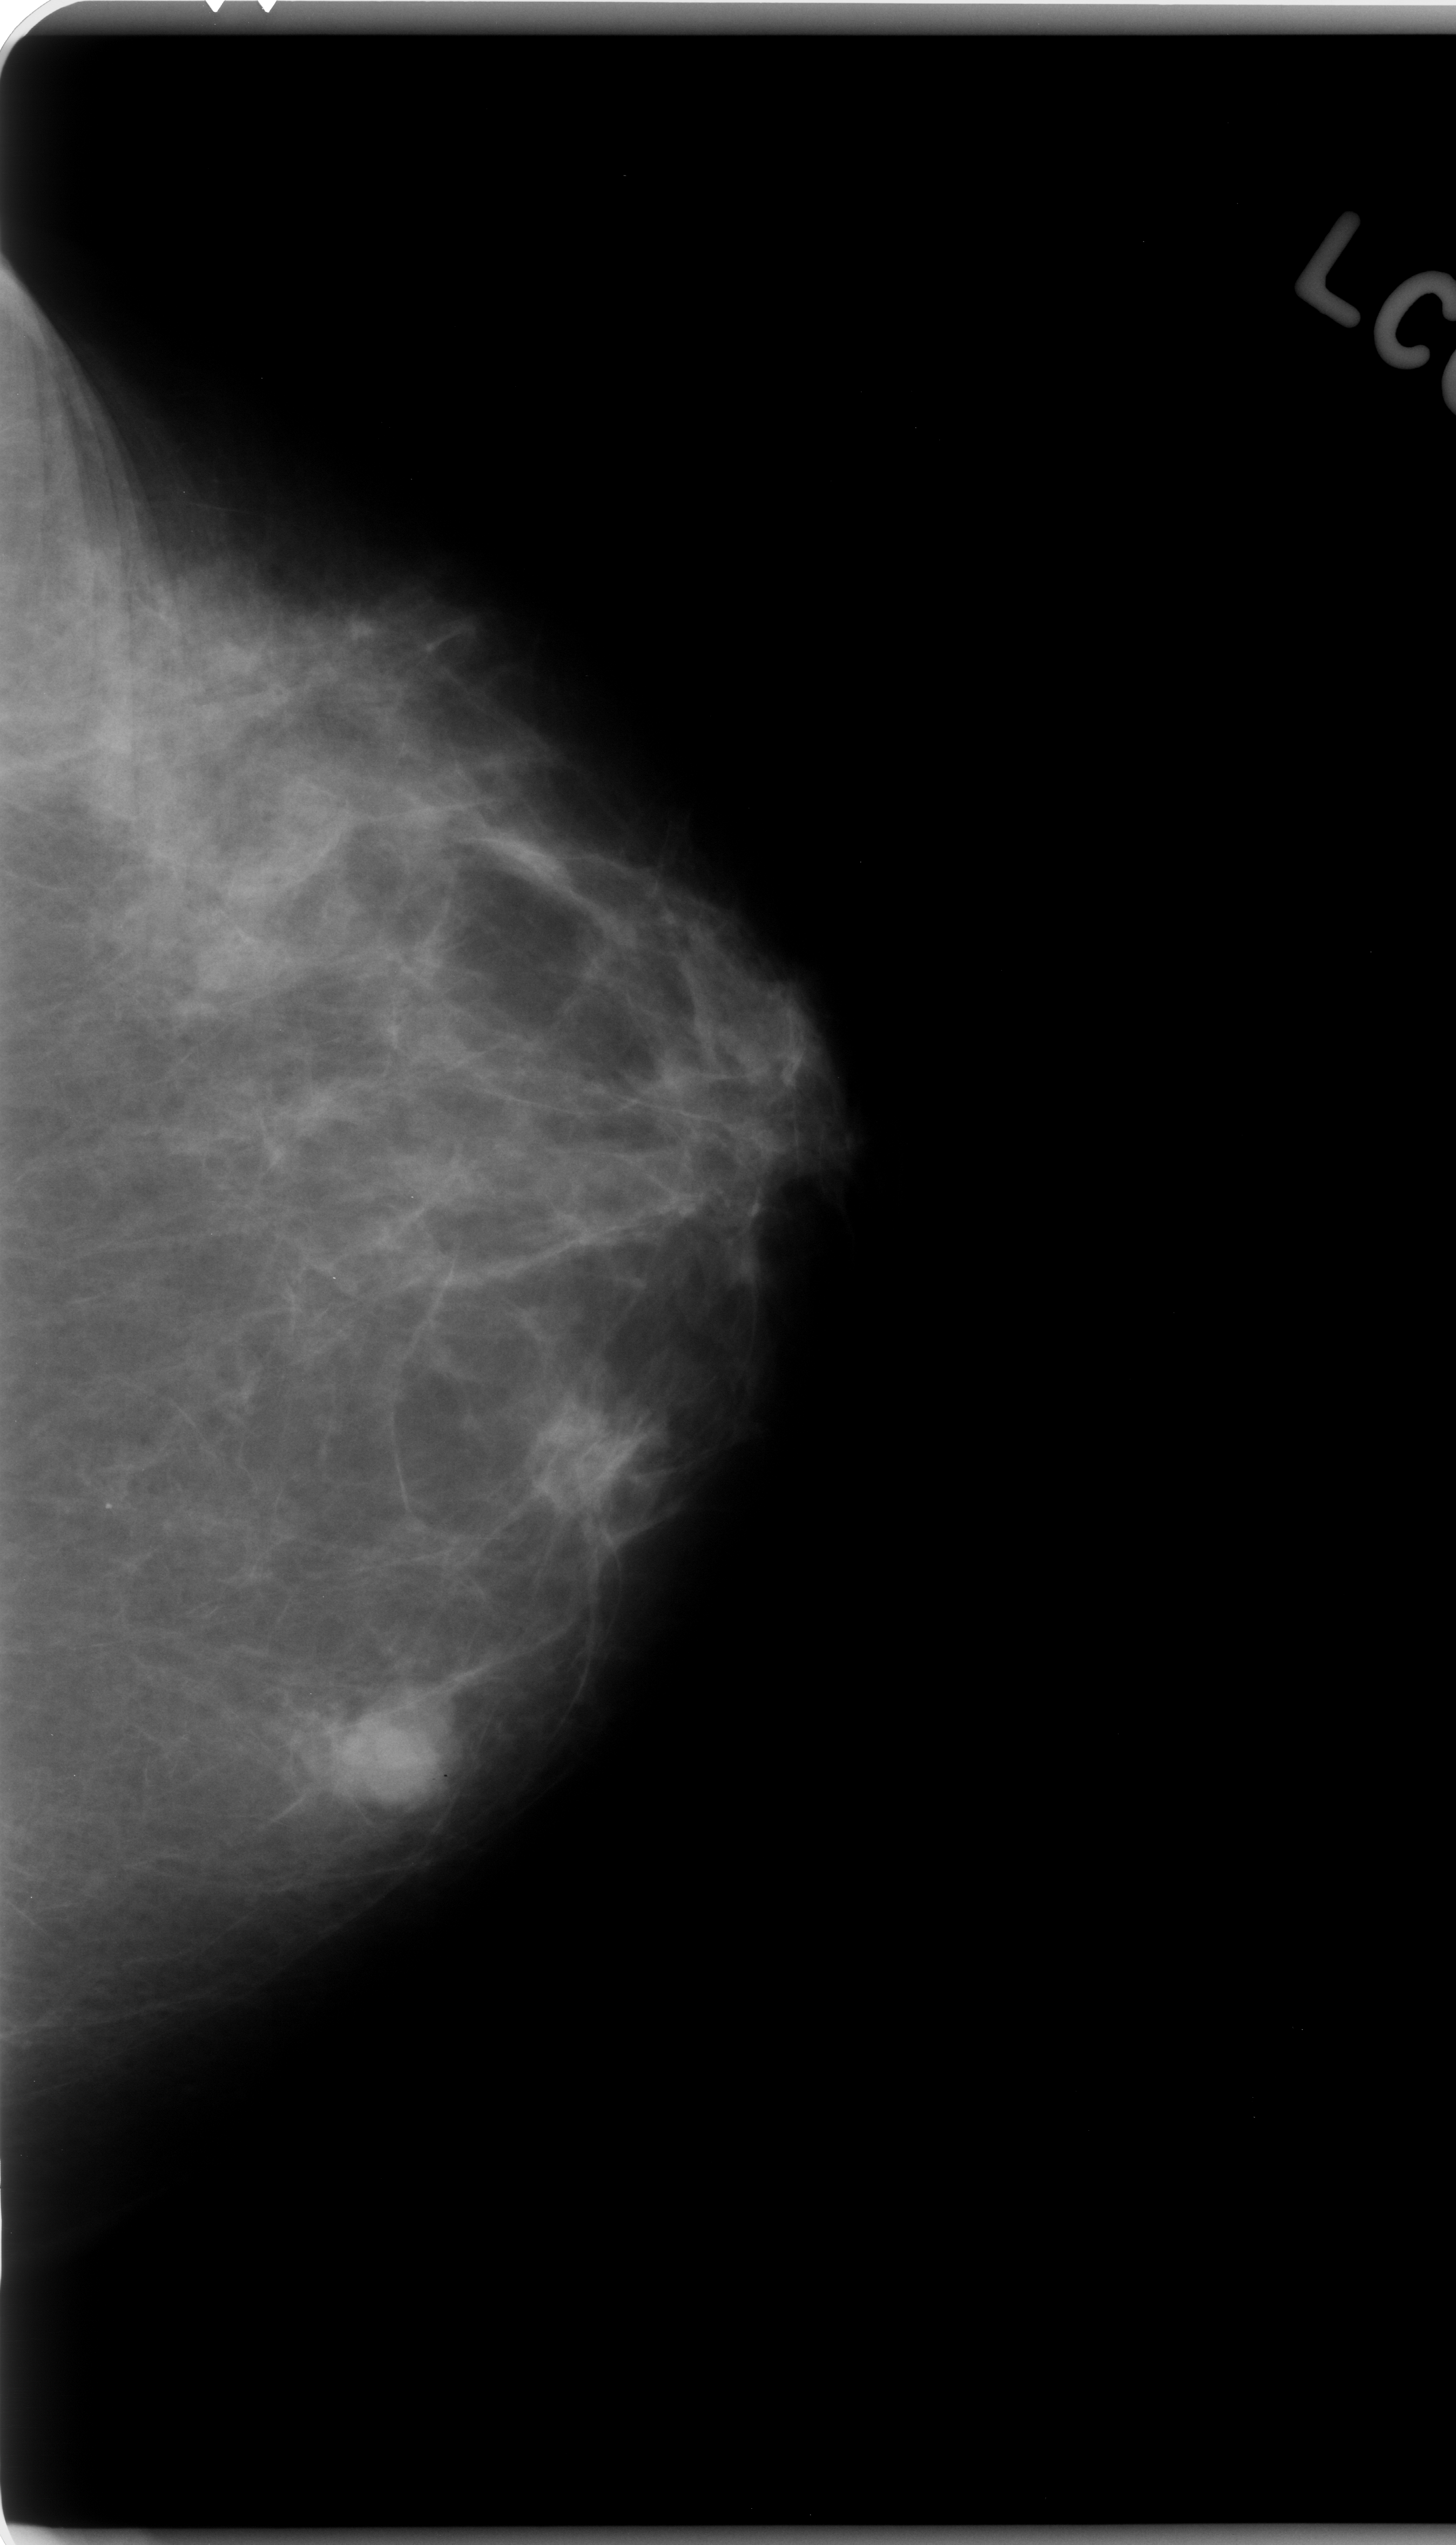
Digitized screen-film mammogram; left breast; craniocaudal (CC) view.
- Abnormality record for this image: mass, shape lobulated, margins microlobulated; BI-RADS assessment category 5; pathology result (as recorded, not read from the image): malignant.